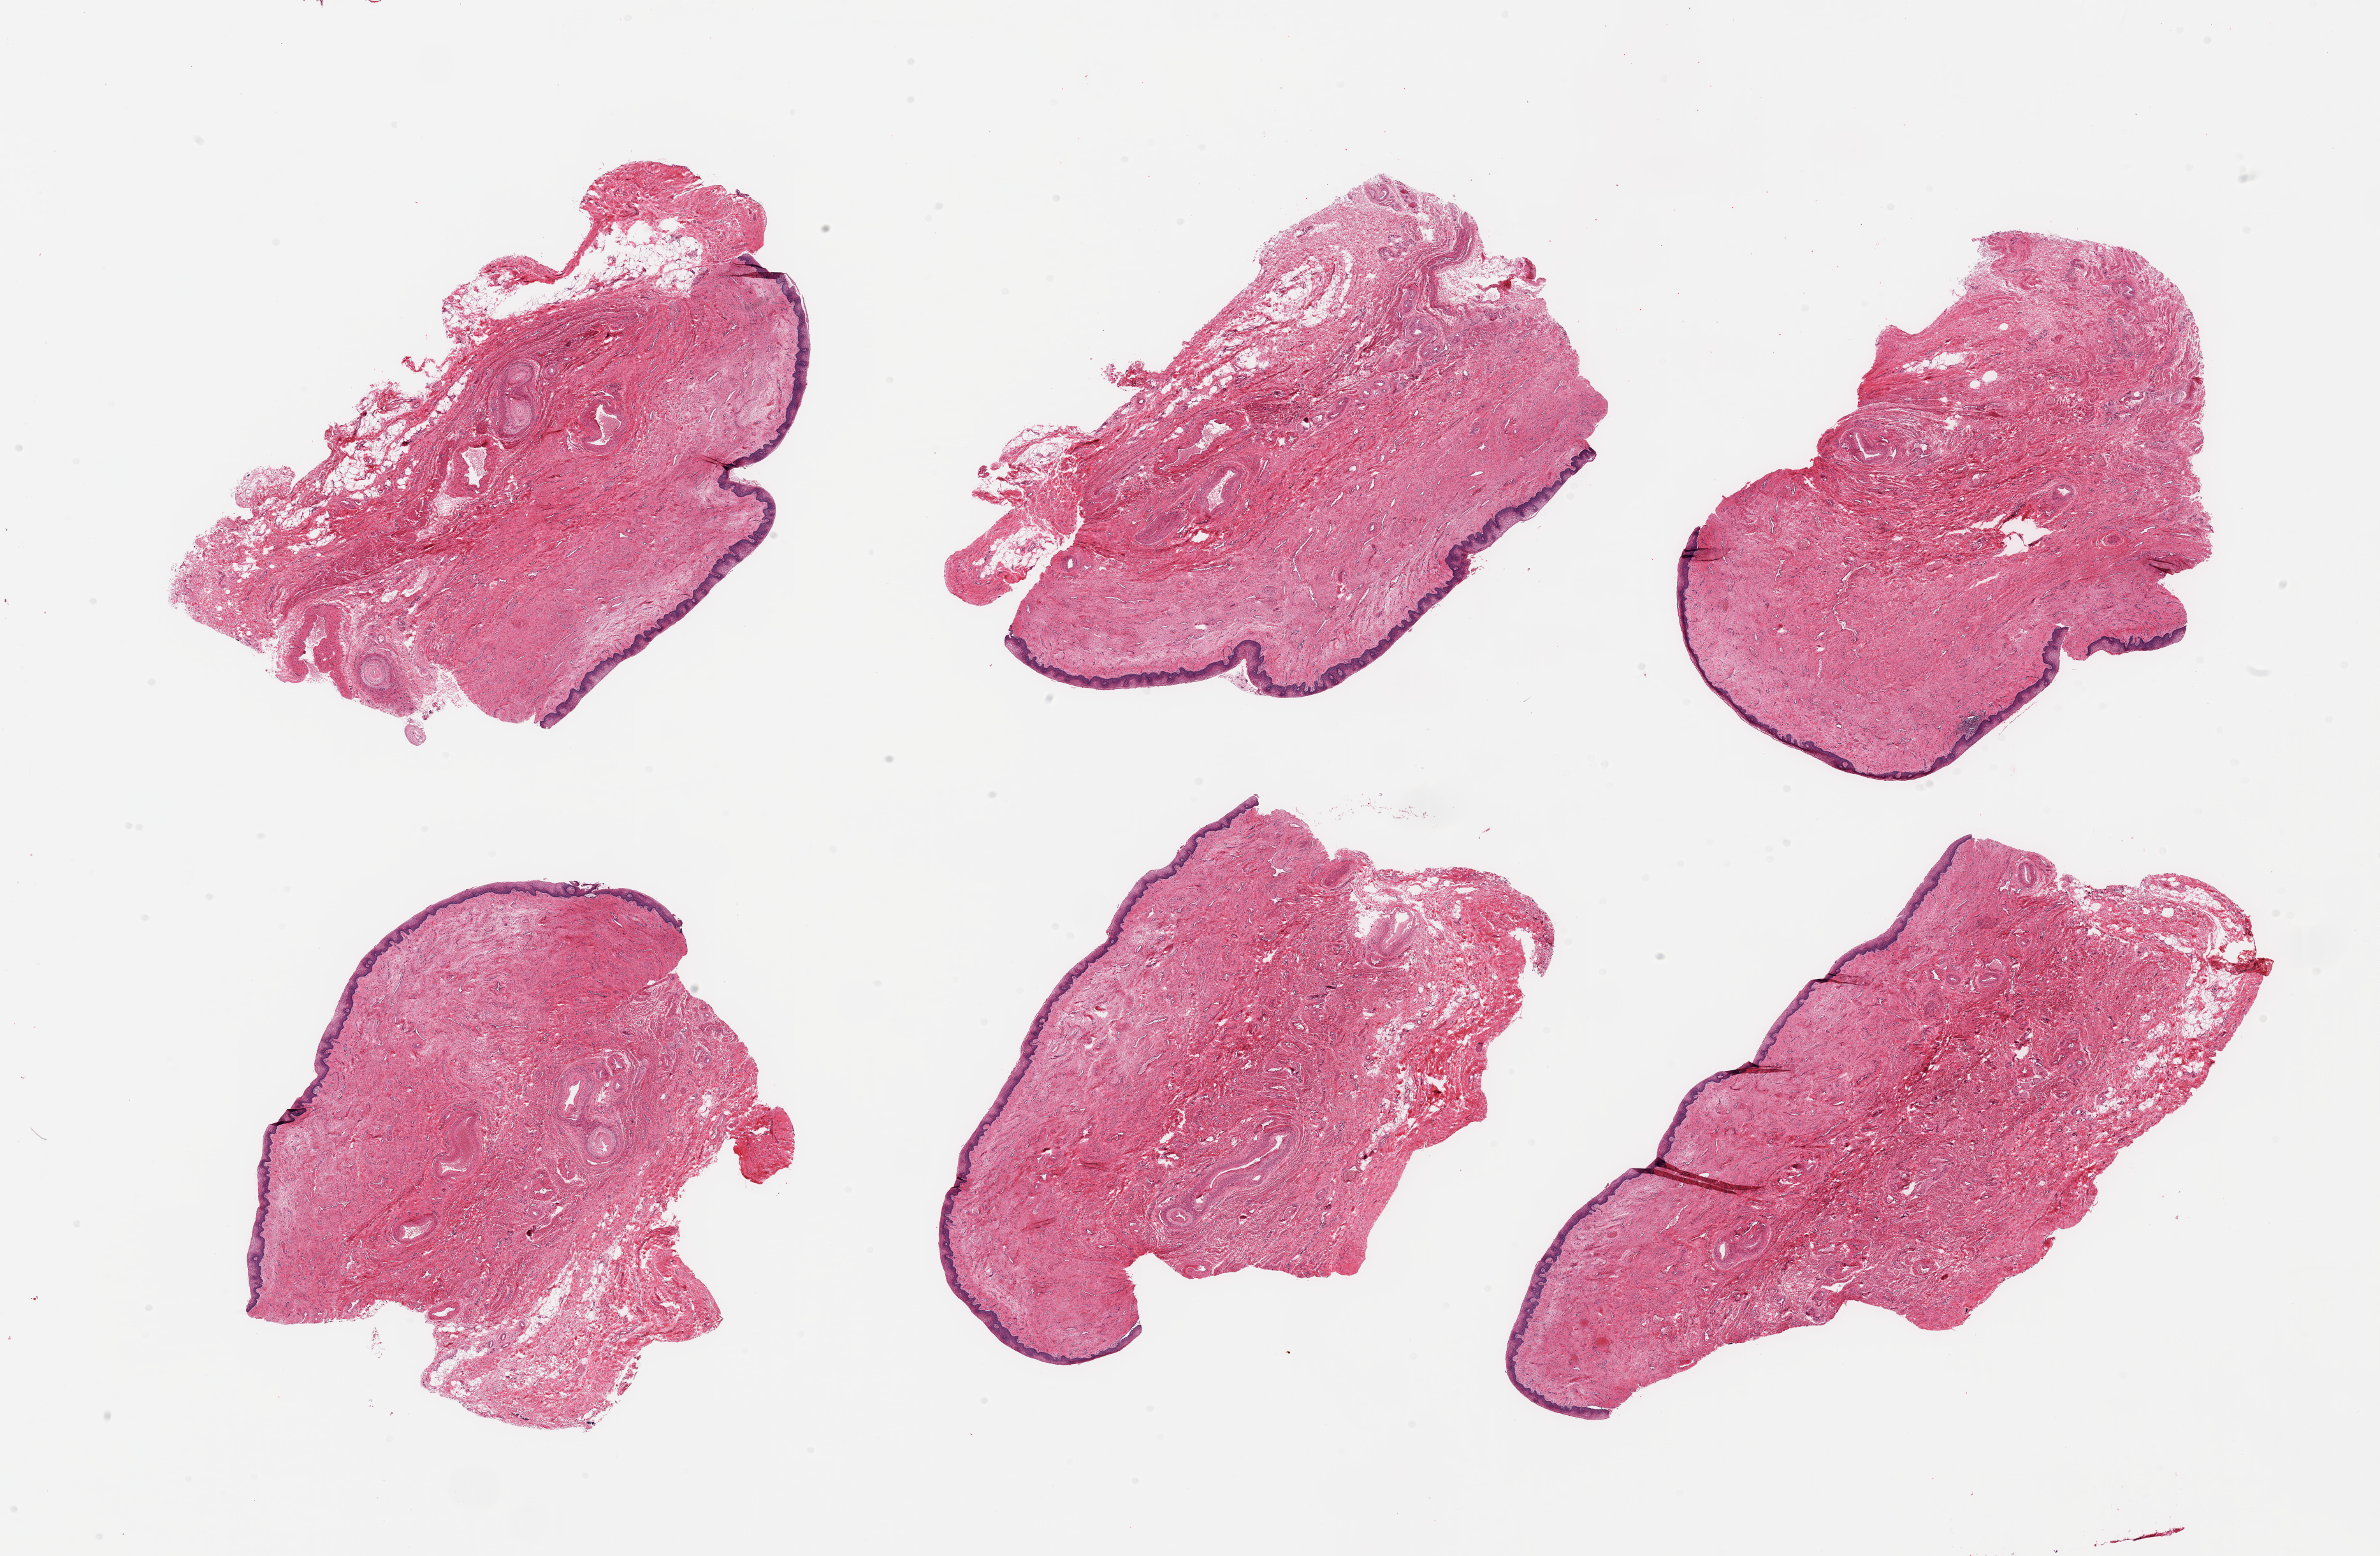
H&E whole-slide image — low-resolution overview of the scanned area, about 29.5 x 19.3 mm; PAXgene-fixed, paraffin-embedded tissue; section of vagina (target tissue); tissue donor sample. Female donor.
Pathologist's review note for this sample: 6 pieces, squamous epithelium up to ~0.2mm.